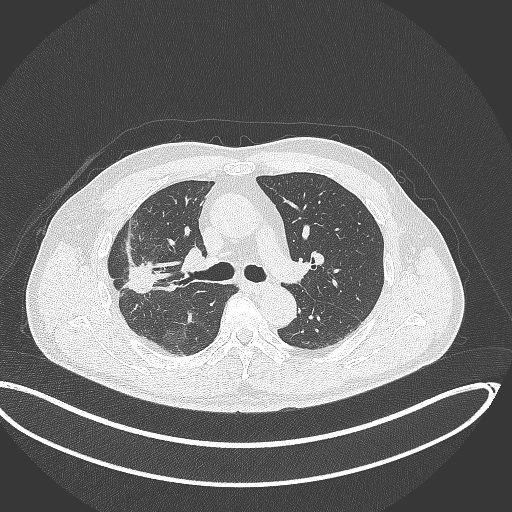
Chest CT, one axial slice; slice 218 of 391 in the series (ordered by position); reconstruction kernel B70f; 120 kVp; lung window (W 1500 / L -600 HU); 1 mm slice thickness; 512 × 512 image matrix, field of view 439 × 439 mm. Patient: male, 63 years. From the clinical record (not read from this slice): clinical TNM (as recorded): T1c N0 M0; histopathological grade: G2-3.
Structures marked on this image (rectangle marked by the reading radiologist):
- lung tumour (recorded histology: adenocarcinoma): bounding box [x1, y1, x2, y2] px = [122, 257, 160, 306]